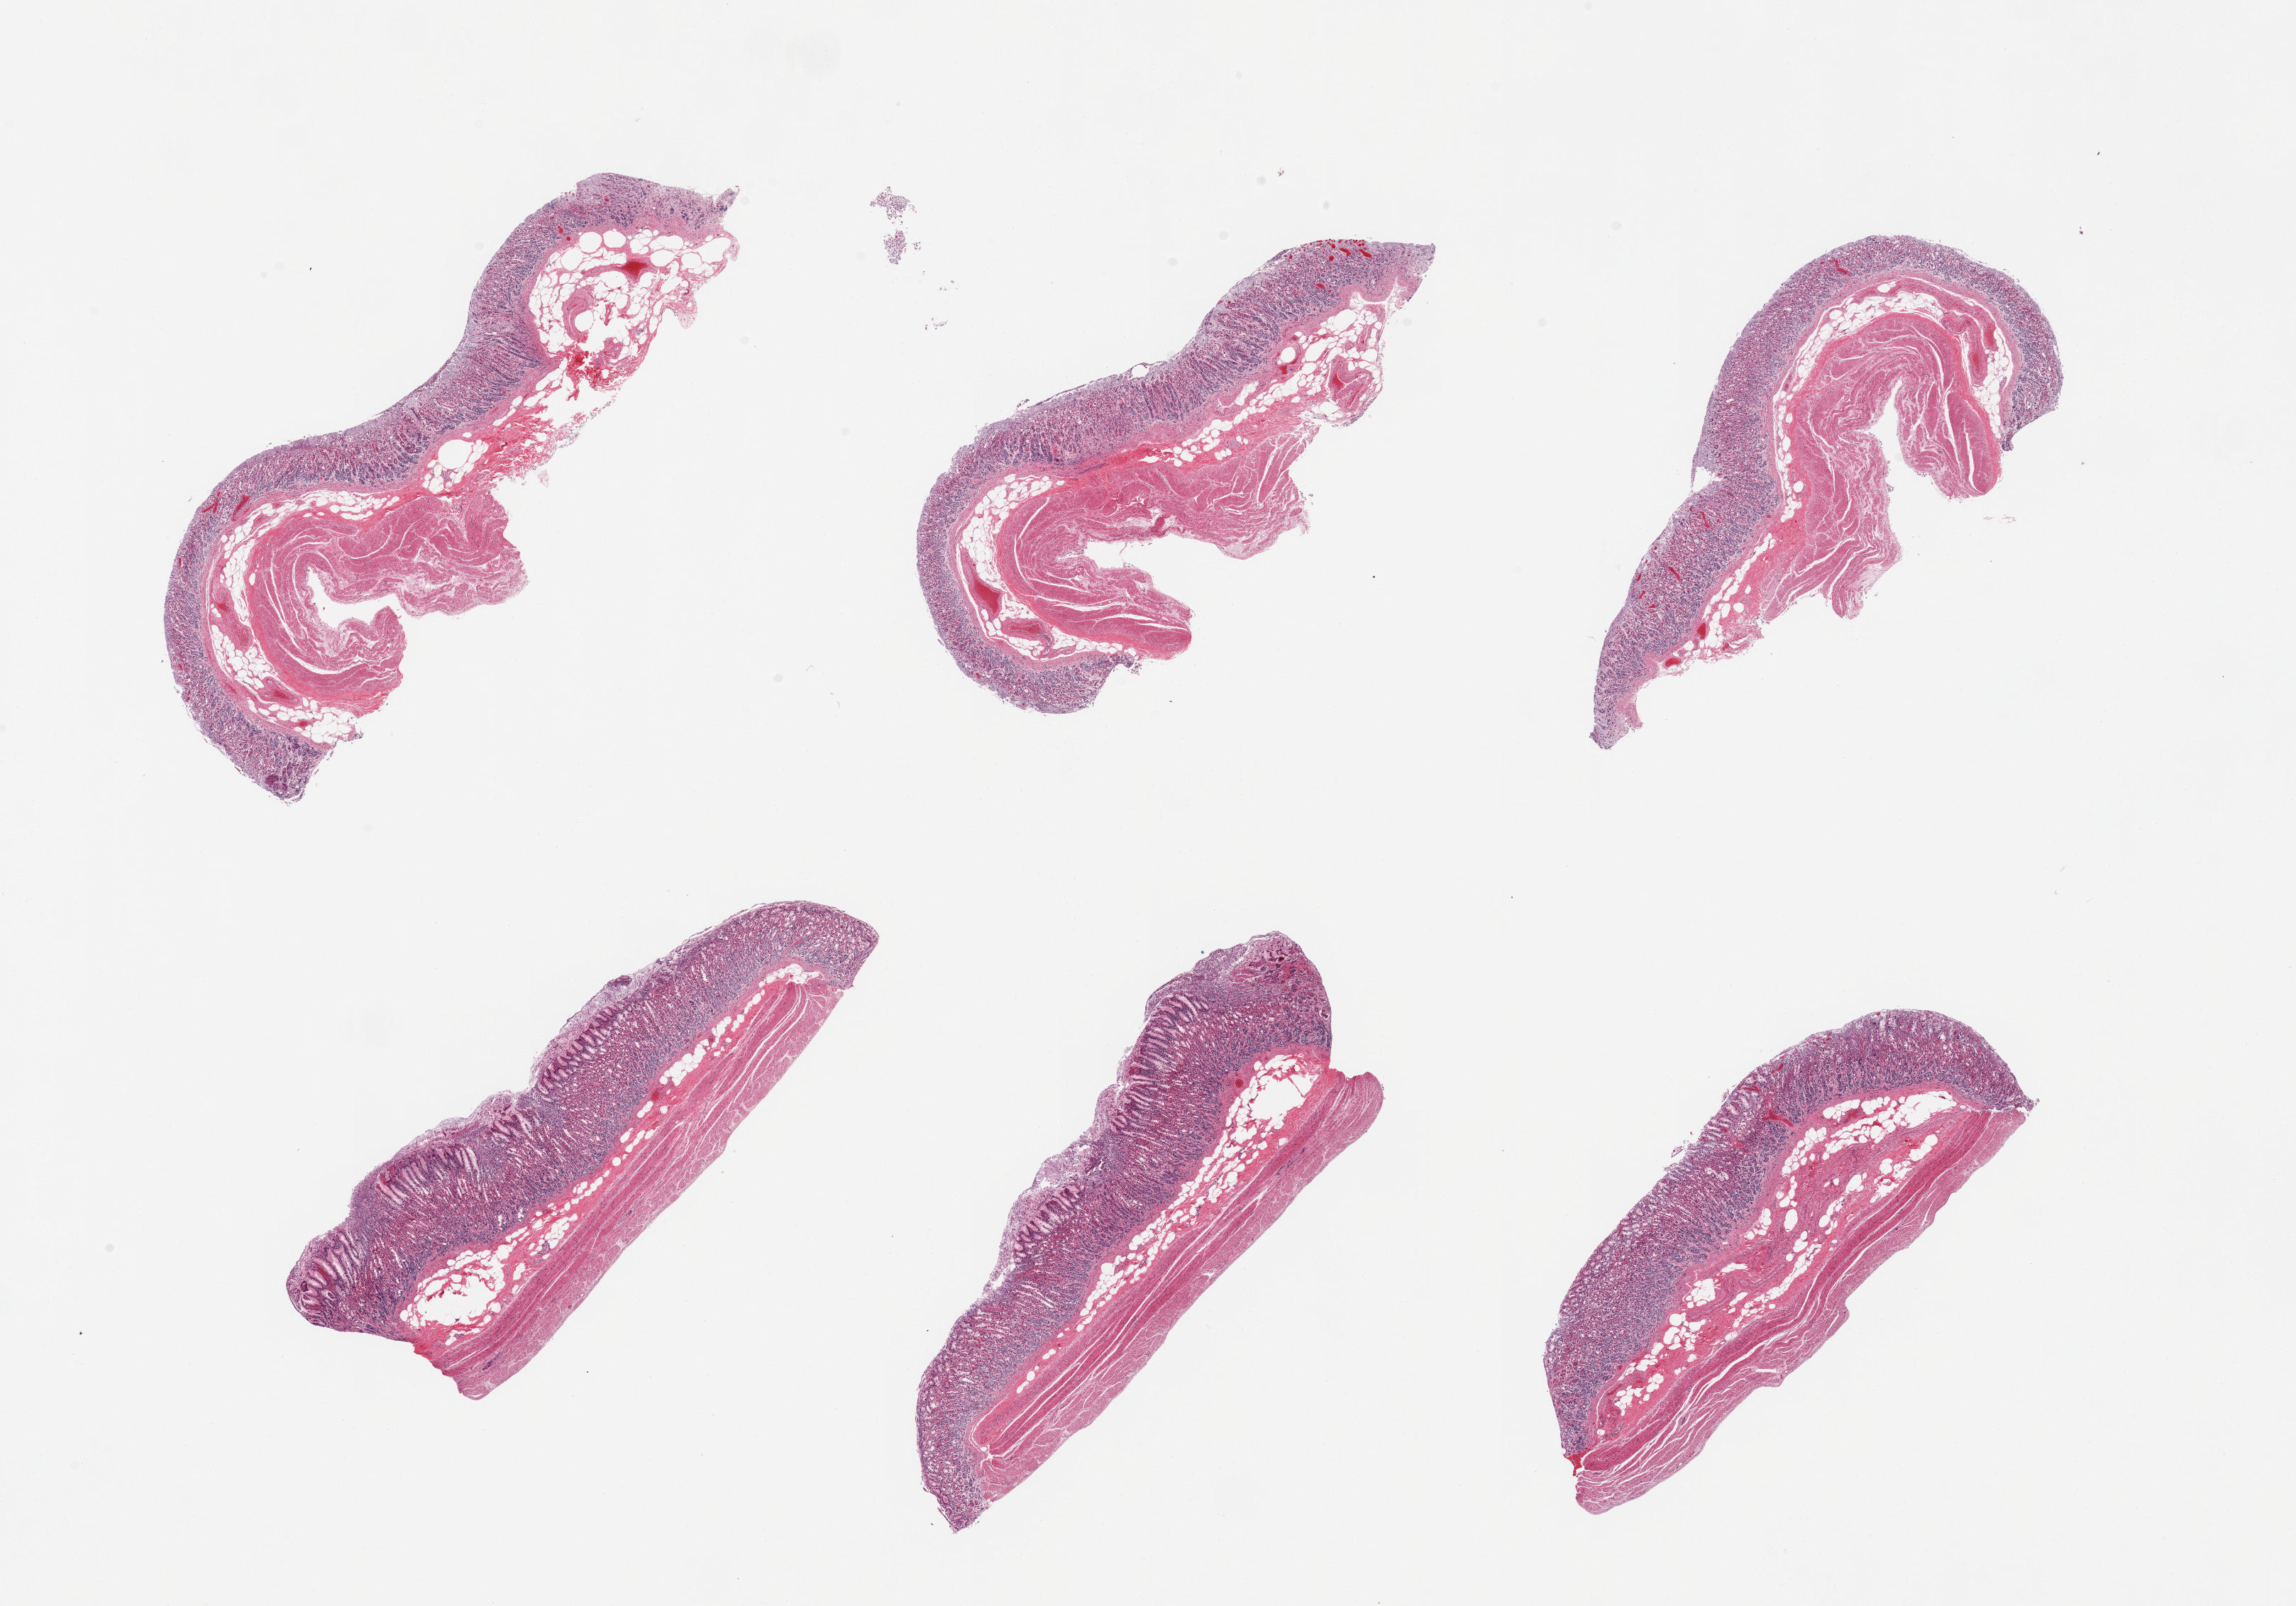
Digitized H&E-stained section, brightfield, a low-resolution overview of the entire scanned area, about 25.6 x 17.9 mm (from a 20x scan); PAXgene-fixed, paraffin-embedded tissue; sampled site (target tissue): stomach; donor tissue sample. Male donor.
Reviewer comment on this tissue sample: 6 pieces; moderately autolyzed mucosa and muscularis; some sloughing of foveolar glands.